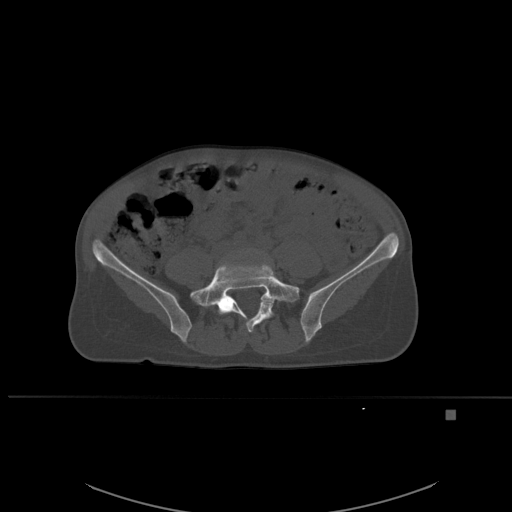
CT including the spine, one axial slice; bone window (W 1800 / L 400 HU); 512 × 512 image matrix, field of view 440 × 440 mm. Patient: female, 45 years. From the clinical record (not read from this slice): primary cancer: lung.
Outlined on this slice (semi-automatic segmentation, software-assisted and operator-edited):
- L4 vertebra: bounding box (x1, y1, x2, y2) in pixels: (243, 249, 249, 253)
- L5 vertebra: (196, 258, 300, 332)